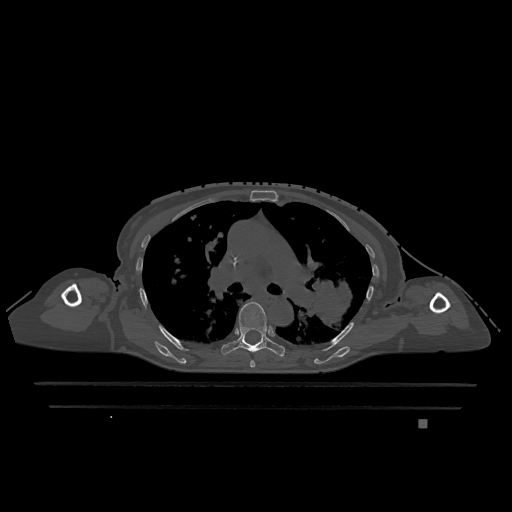
CT including the spine, one axial slice. Slice 796 of 1317 in the series (ordered by position). Bone window (W 1800 / L 400 HU). 0.5 mm slice thickness. 512 × 512 image matrix. Patient: female, 74 years. From the clinical record (not read from this slice): primary cancer: lung.
Outlined on this slice (semi-automatically segmented with operator editing):
- T5 vertebra: bounding box [x1, y1, x2, y2] px = [250, 360, 255, 368]
- T6 vertebra: [221, 302, 285, 357]